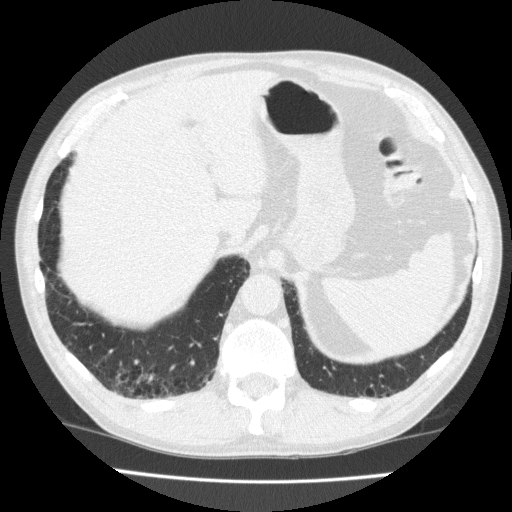
Axial slice from a low-dose chest CT screening exam, first (baseline) screen, lung window (W 1500 / L -600 HU), 120 kVp, 512 × 512 image matrix, field of view 356 × 356 mm. Male, age 70 years at enrolment. Current smoker at enrolment.
Expert reader's lesion annotation, bounding box [x1, y1, x2, y2] px = [118, 359, 171, 400]. Screening reader's record for this exam: no non-calcified nodule ≥4 mm recorded. Official screen result: negative screen, significant abnormalities not suspicious for lung cancer.